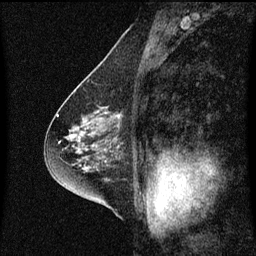
Breast MRI (dynamic contrast-enhanced), one sagittal slice. Position 36 of 60 along the scan axis. Dynamic contrast-enhanced series, image 2 of 3 at this slice position (ordered by acquisition). 1.5 T. TE 4.2 ms, TR 8.4 ms. 2 mm slice thickness. 256 × 256 image matrix, field of view 200 × 200 mm. Patient: female, 58 years.
Structures marked on this image (semi-automatically segmented with operator editing):
- analysis volume of interest (the breast-tissue region the enhancement analysis was run in; not a lesion): bounding box (x1, y1, x2, y2) in pixels: (86, 104, 124, 143)
- tumour enhancement mask (voxels above the 70 % enhancement threshold inside the analysis volume of interest): (104, 108, 120, 127)